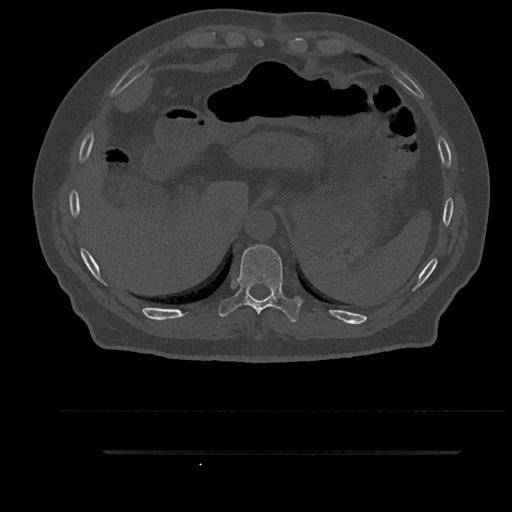
CT including the spine, one axial slice. Position 371 of 797 along the scan axis. Reconstruction kernel Br40s/3. 120 kVp. Bone window (W 1800 / L 400 HU). 0.5 mm slice thickness. 512 × 512 image matrix. Patient: male, 63 years. Case-level facts recorded for this patient, not image findings: primary cancer: renal; vertebrae with lytic lesions (as recorded): T8.
Annotated regions visible in this slice (semi-automatically segmented with operator editing):
- T10 vertebra: bounding box (x1, y1, x2, y2) in pixels: (218, 245, 302, 322)